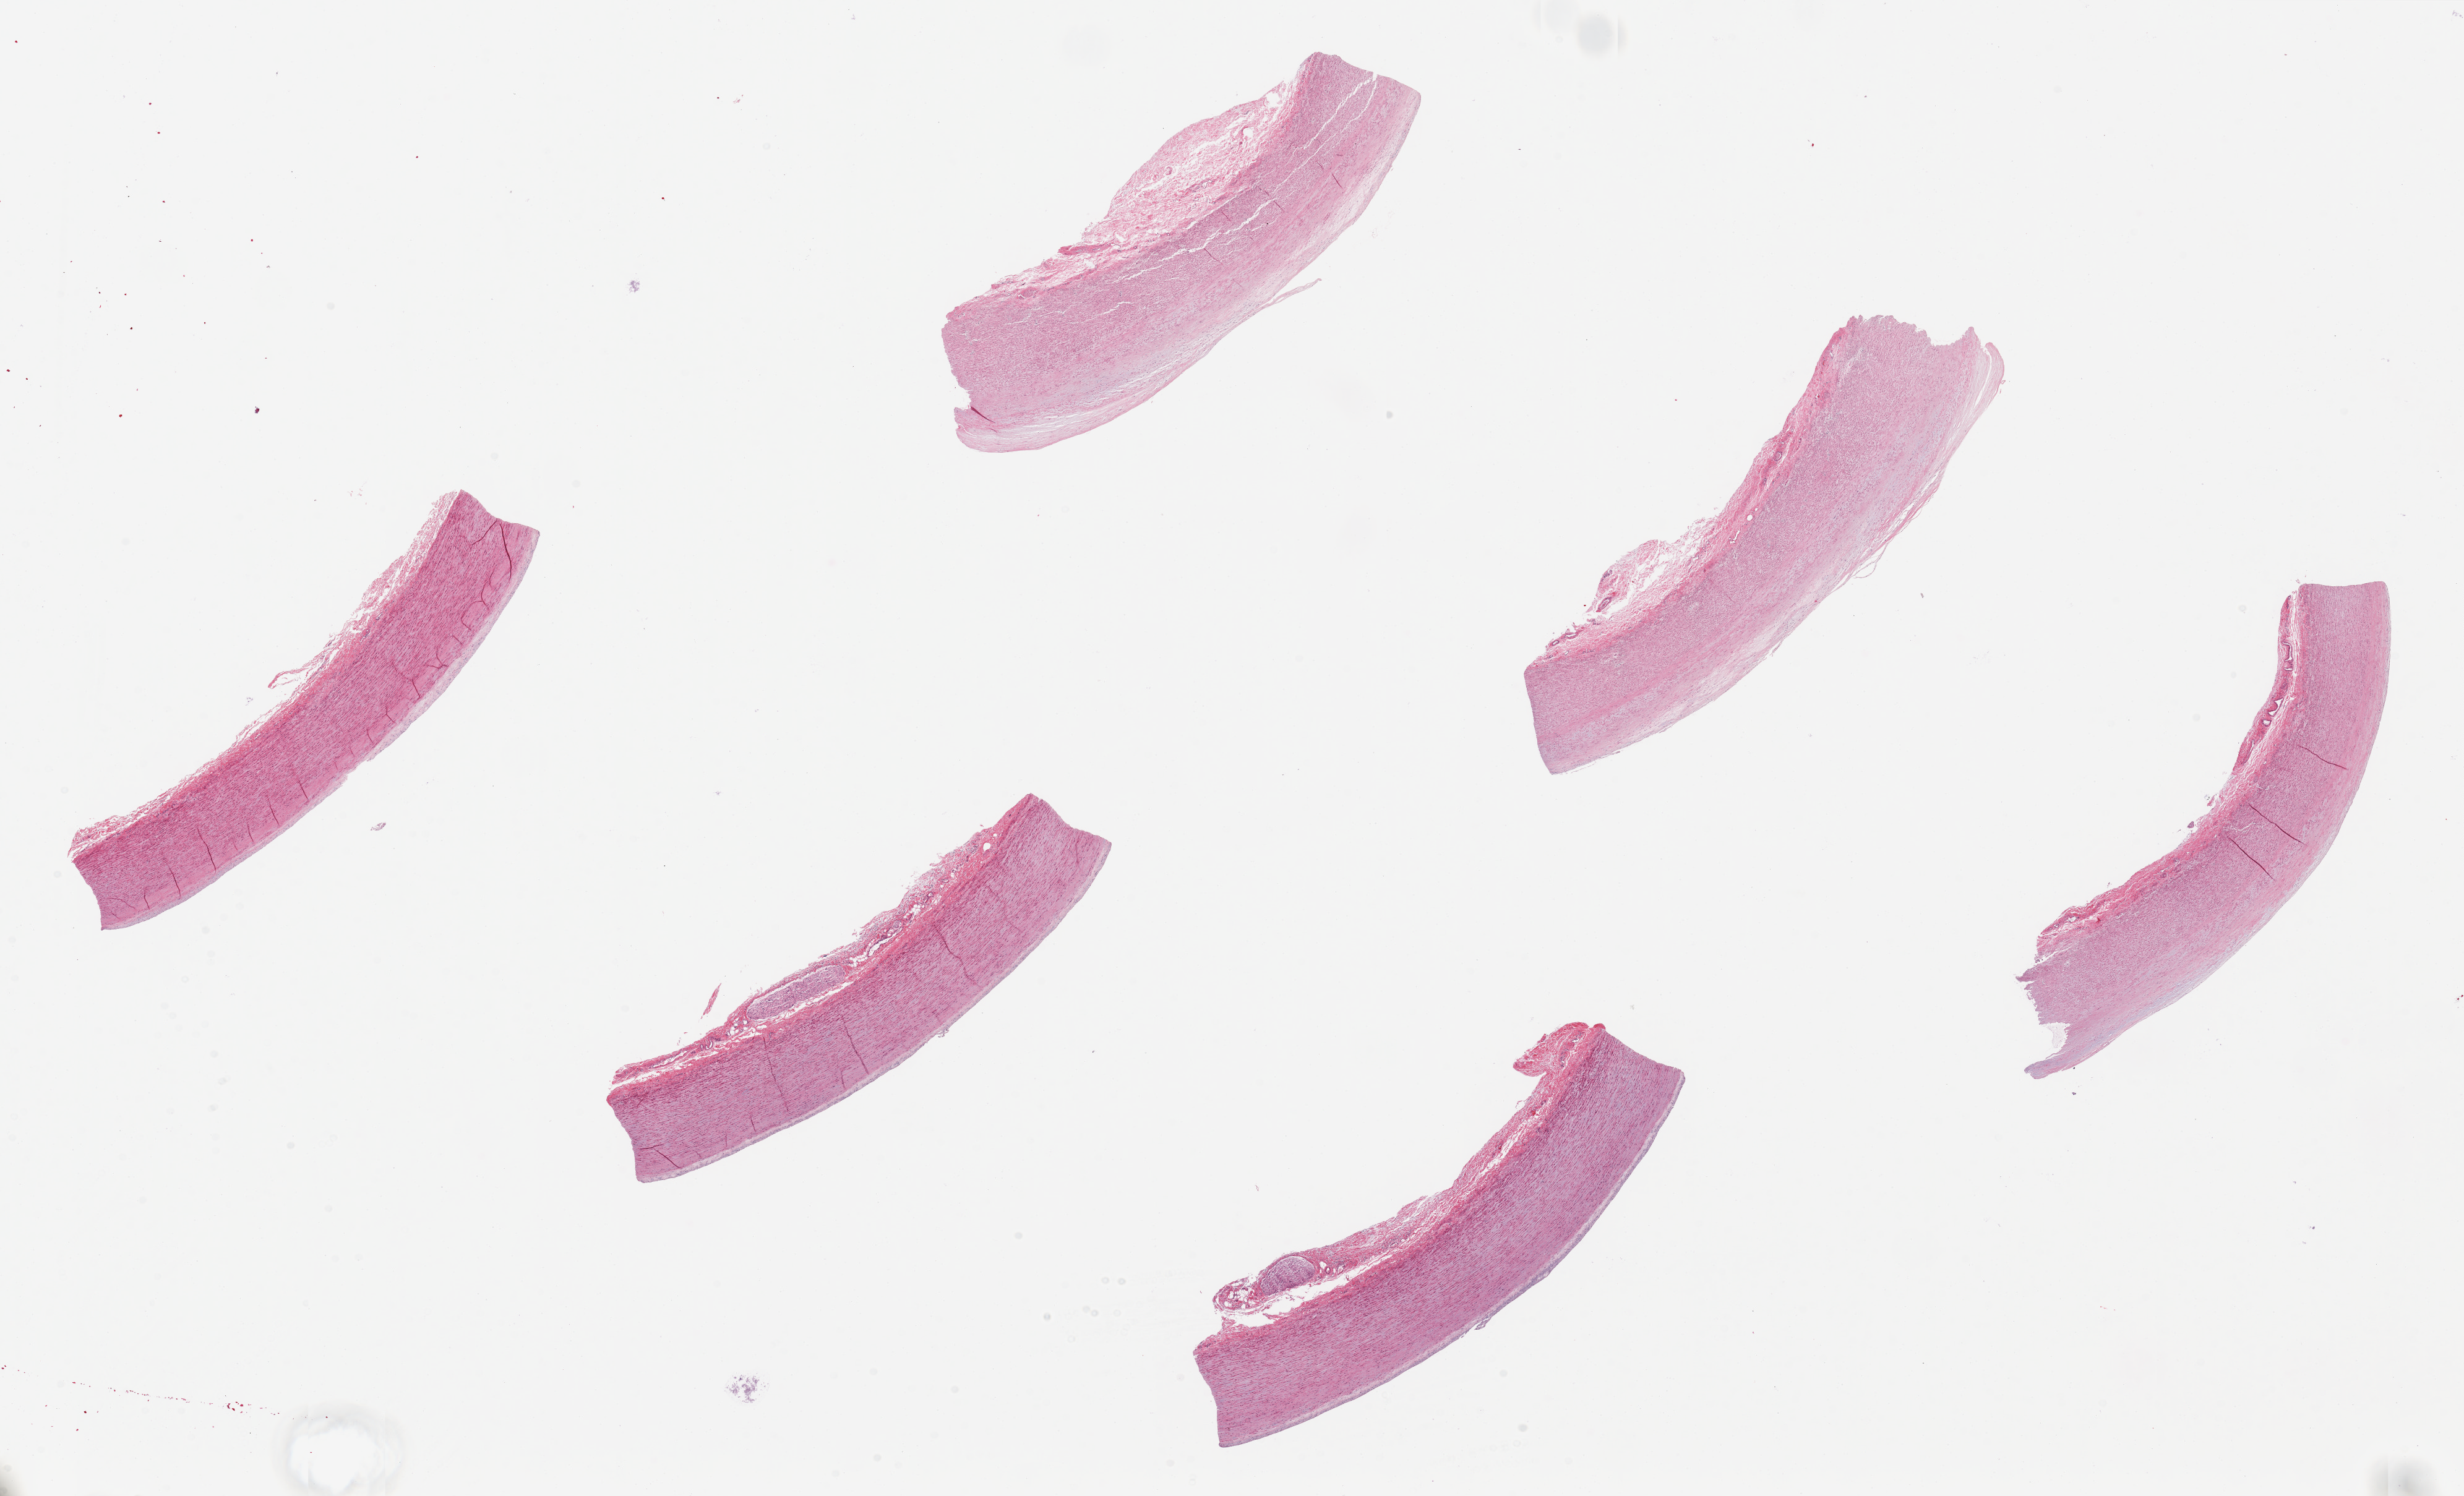
Digitized haematoxylin and eosin-stained section — shown as a low-resolution overview of the whole scanned area (about 31.5 x 19.1 mm, from a 20x scan). PAXgene-fixed, paraffin-embedded tissue. Section of aorta (target tissue). Tissue donor sample. Donor sex: female.
Reviewer comment on this tissue sample: 6 pieces, up to 8x2mm; adherent advential fat up to ~0.5mm thick.